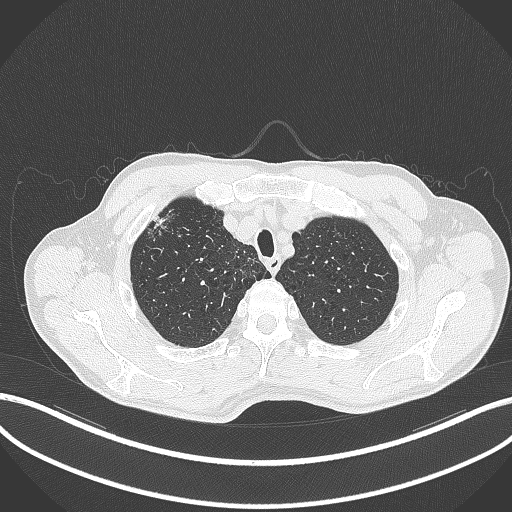
Chest CT, one axial slice; slice 362 of 427 in the series (ordered by position); lung window (W 1500 / L -600 HU); 512 × 512 image matrix. Patient: male, 69 years. Case-level facts recorded for this patient, not image findings: clinical TNM (as recorded): T1b N1 M0.
Outlined on this slice (rectangle marked by the reading radiologist):
- lung tumour (recorded histology: adenocarcinoma): bounding box (x1, y1, x2, y2) in pixels: (152, 211, 173, 236)